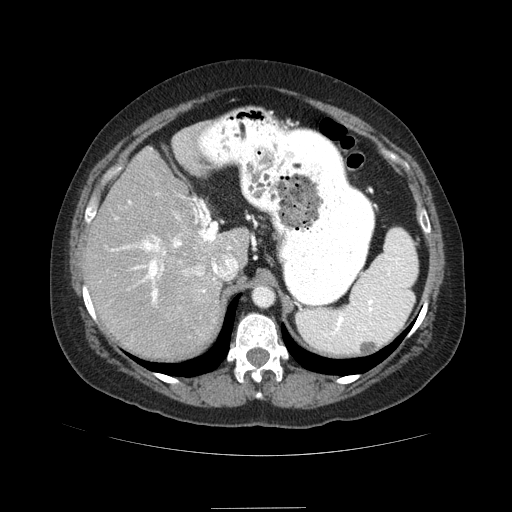
Contrast-enhanced abdominal CT (liver protocol), one axial slice; reconstruction kernel STANDARD; soft-tissue window (W 400 / L 40 HU); 2.5 mm slice thickness; 512 × 512 image matrix, field of view 400 × 400 mm. From the clinical record (not read from this slice): diagnosis: hepatocellular carcinoma (patient treated with transarterial chemoembolisation; whether this scan precedes or follows treatment is not stated here); TNM stage (as recorded): Stage-IIIB; Child-Pugh class: A; tumour nodularity: multinodular.
Annotated regions visible in this slice (semi-automatic segmentation, software-assisted and operator-edited):
- abdominal aorta: bounding box [x1, y1, x2, y2] px = [254, 285, 273, 306]
- liver parenchyma outside the tumour (the mass and vessels are separate outlines, so this box may not span the whole liver): [83, 124, 250, 360]
- liver vessels: [111, 198, 236, 304]